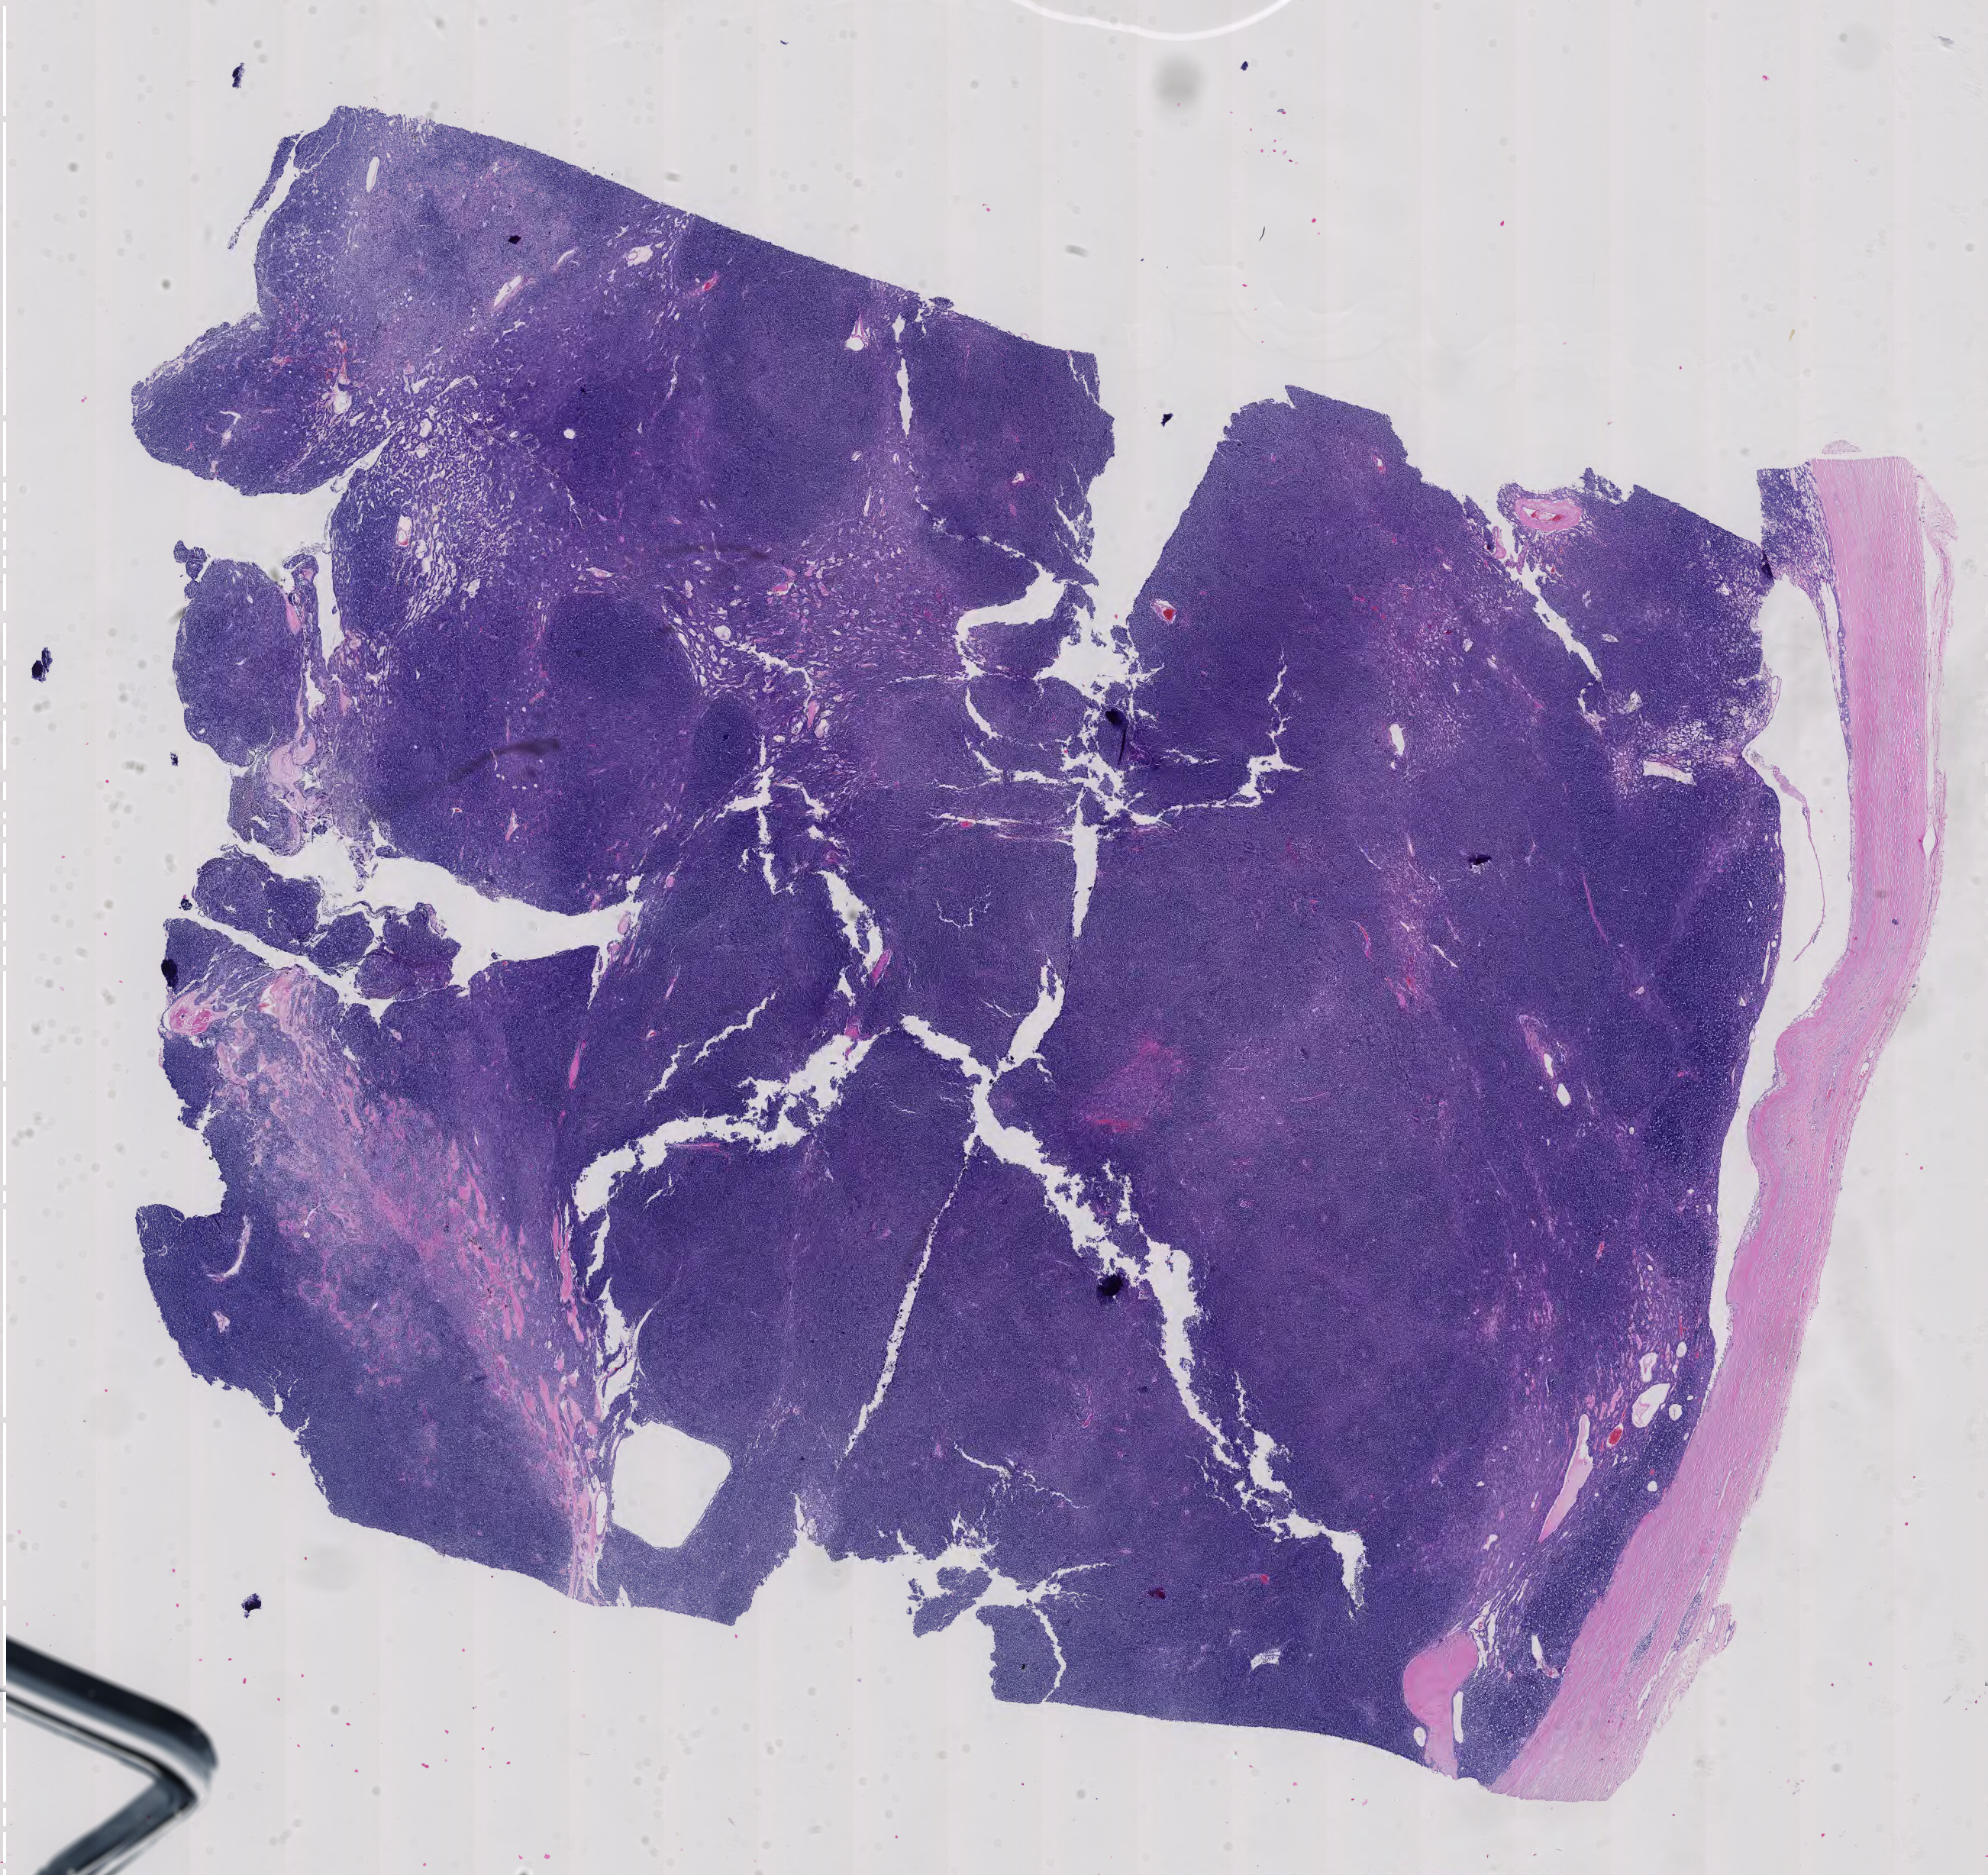
Whole-slide histology image, H&E-stained — a low-resolution overview of the entire scanned area, about 19.0 x 17.9 mm, FFPE section, primary tumour sample from the thymus. Male, age 53 years at initial diagnosis.
• diagnosis: Thymoma, type B2, malignant (anterior mediastinum)